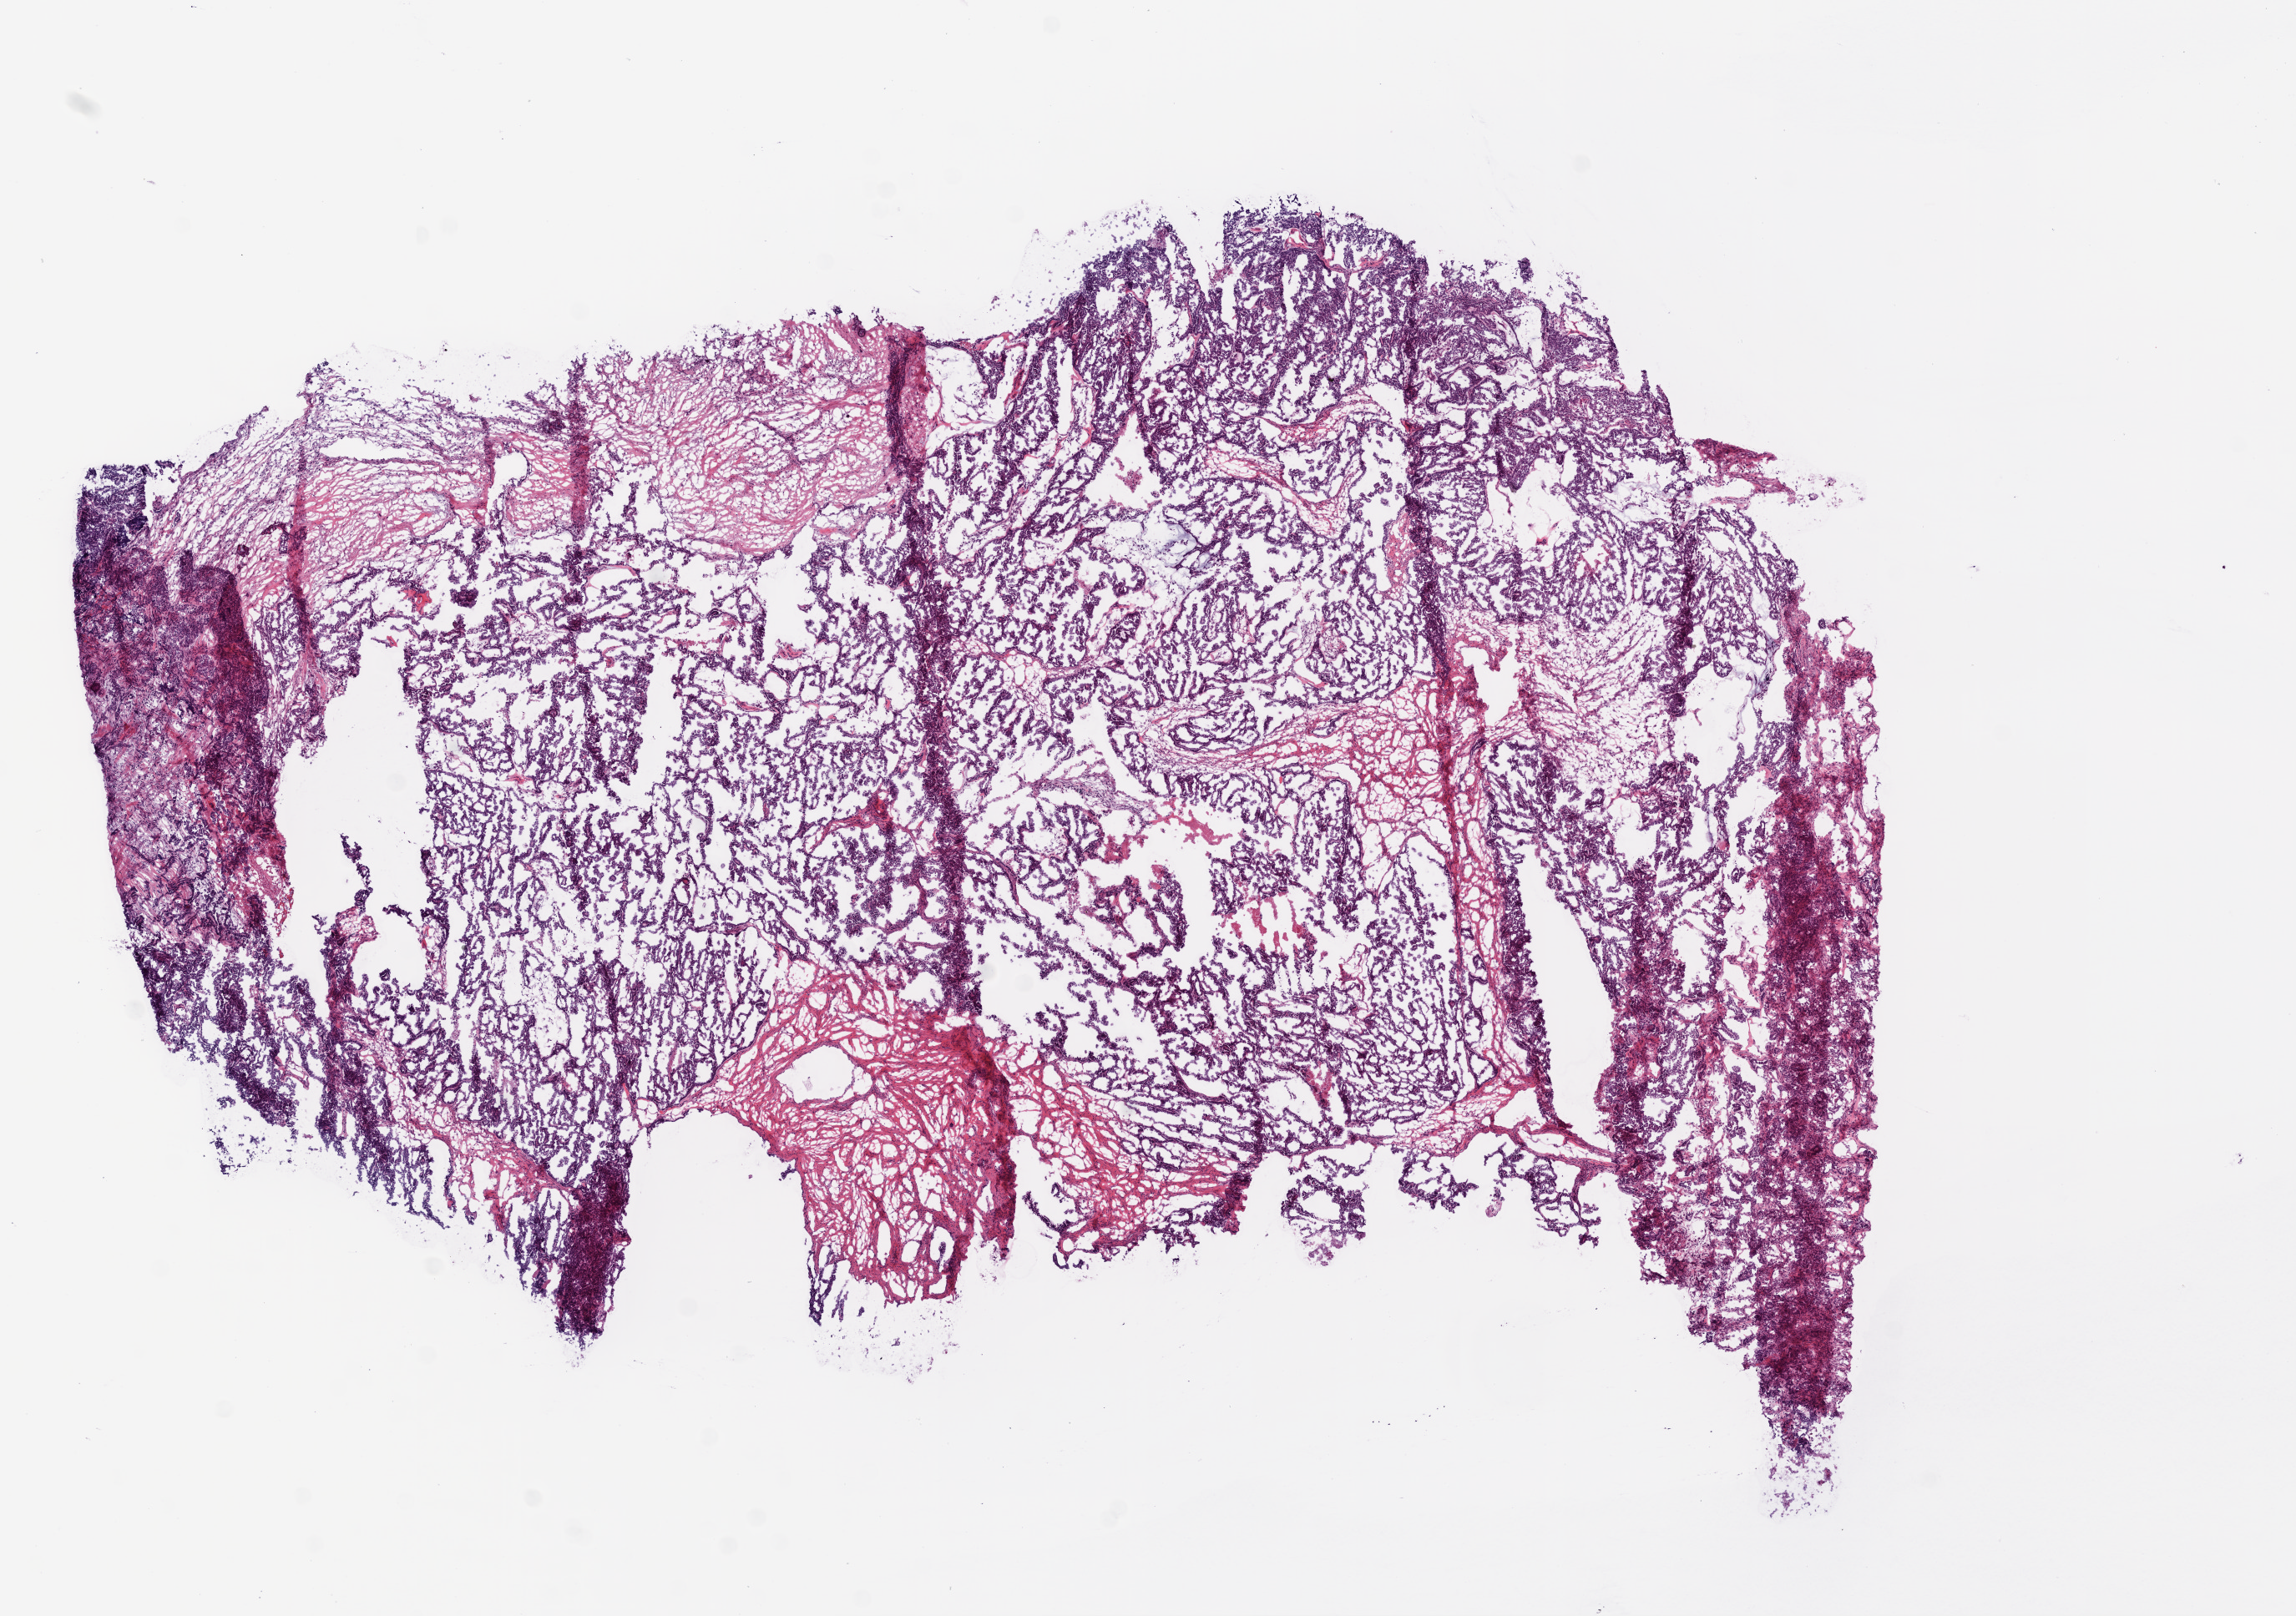
Digitized Hematoxylin and eosin (H&E) stained tissue section (whole slide), low-resolution overview of the scanned area, about 11.0 x 7.8 mm (acquisition: 20x scan). Frozen section from the top of the tissue portion. Sample: primary tumour, ovary. Female patient; age at initial diagnosis 48 years. Histologic grade: G3 (poorly differentiated). Slide review estimates, as recorded: tumour cells 80%, tumour nuclei 90%, normal cells 0%, stromal cells 15%, necrosis 5%.
Laterality: bilateral. FIGO stage: IIIC. Histologic diagnosis: Serous cystadenocarcinoma, NOS.